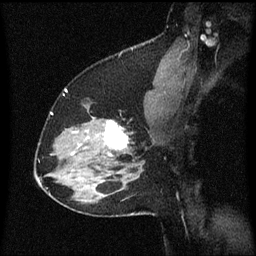
Breast MRI (dynamic contrast-enhanced), one sagittal slice. Slice 44 of 60 in the series (ordered by position). Dynamic contrast-enhanced series, image 2 of 3 at this slice position (ordered by acquisition). 1.5 T. TE 4.2 ms, TR 8.4 ms. 256 × 256 image matrix. Female patient, age 37 years. Case-level facts recorded for this patient, not image findings: setting: breast cancer imaged before/during neoadjuvant chemotherapy; receptor status: HR-positive, HER2-negative.
Structures marked on this image (semi-automatically segmented with operator editing):
- analysis volume of interest (the breast-tissue region the enhancement analysis was run in; not a lesion): box from (x=94, y=118) to (x=135, y=157) px
- tumour enhancement mask (voxels above the 70 % enhancement threshold inside the analysis volume of interest): (x=105, y=122)–(x=129, y=157)